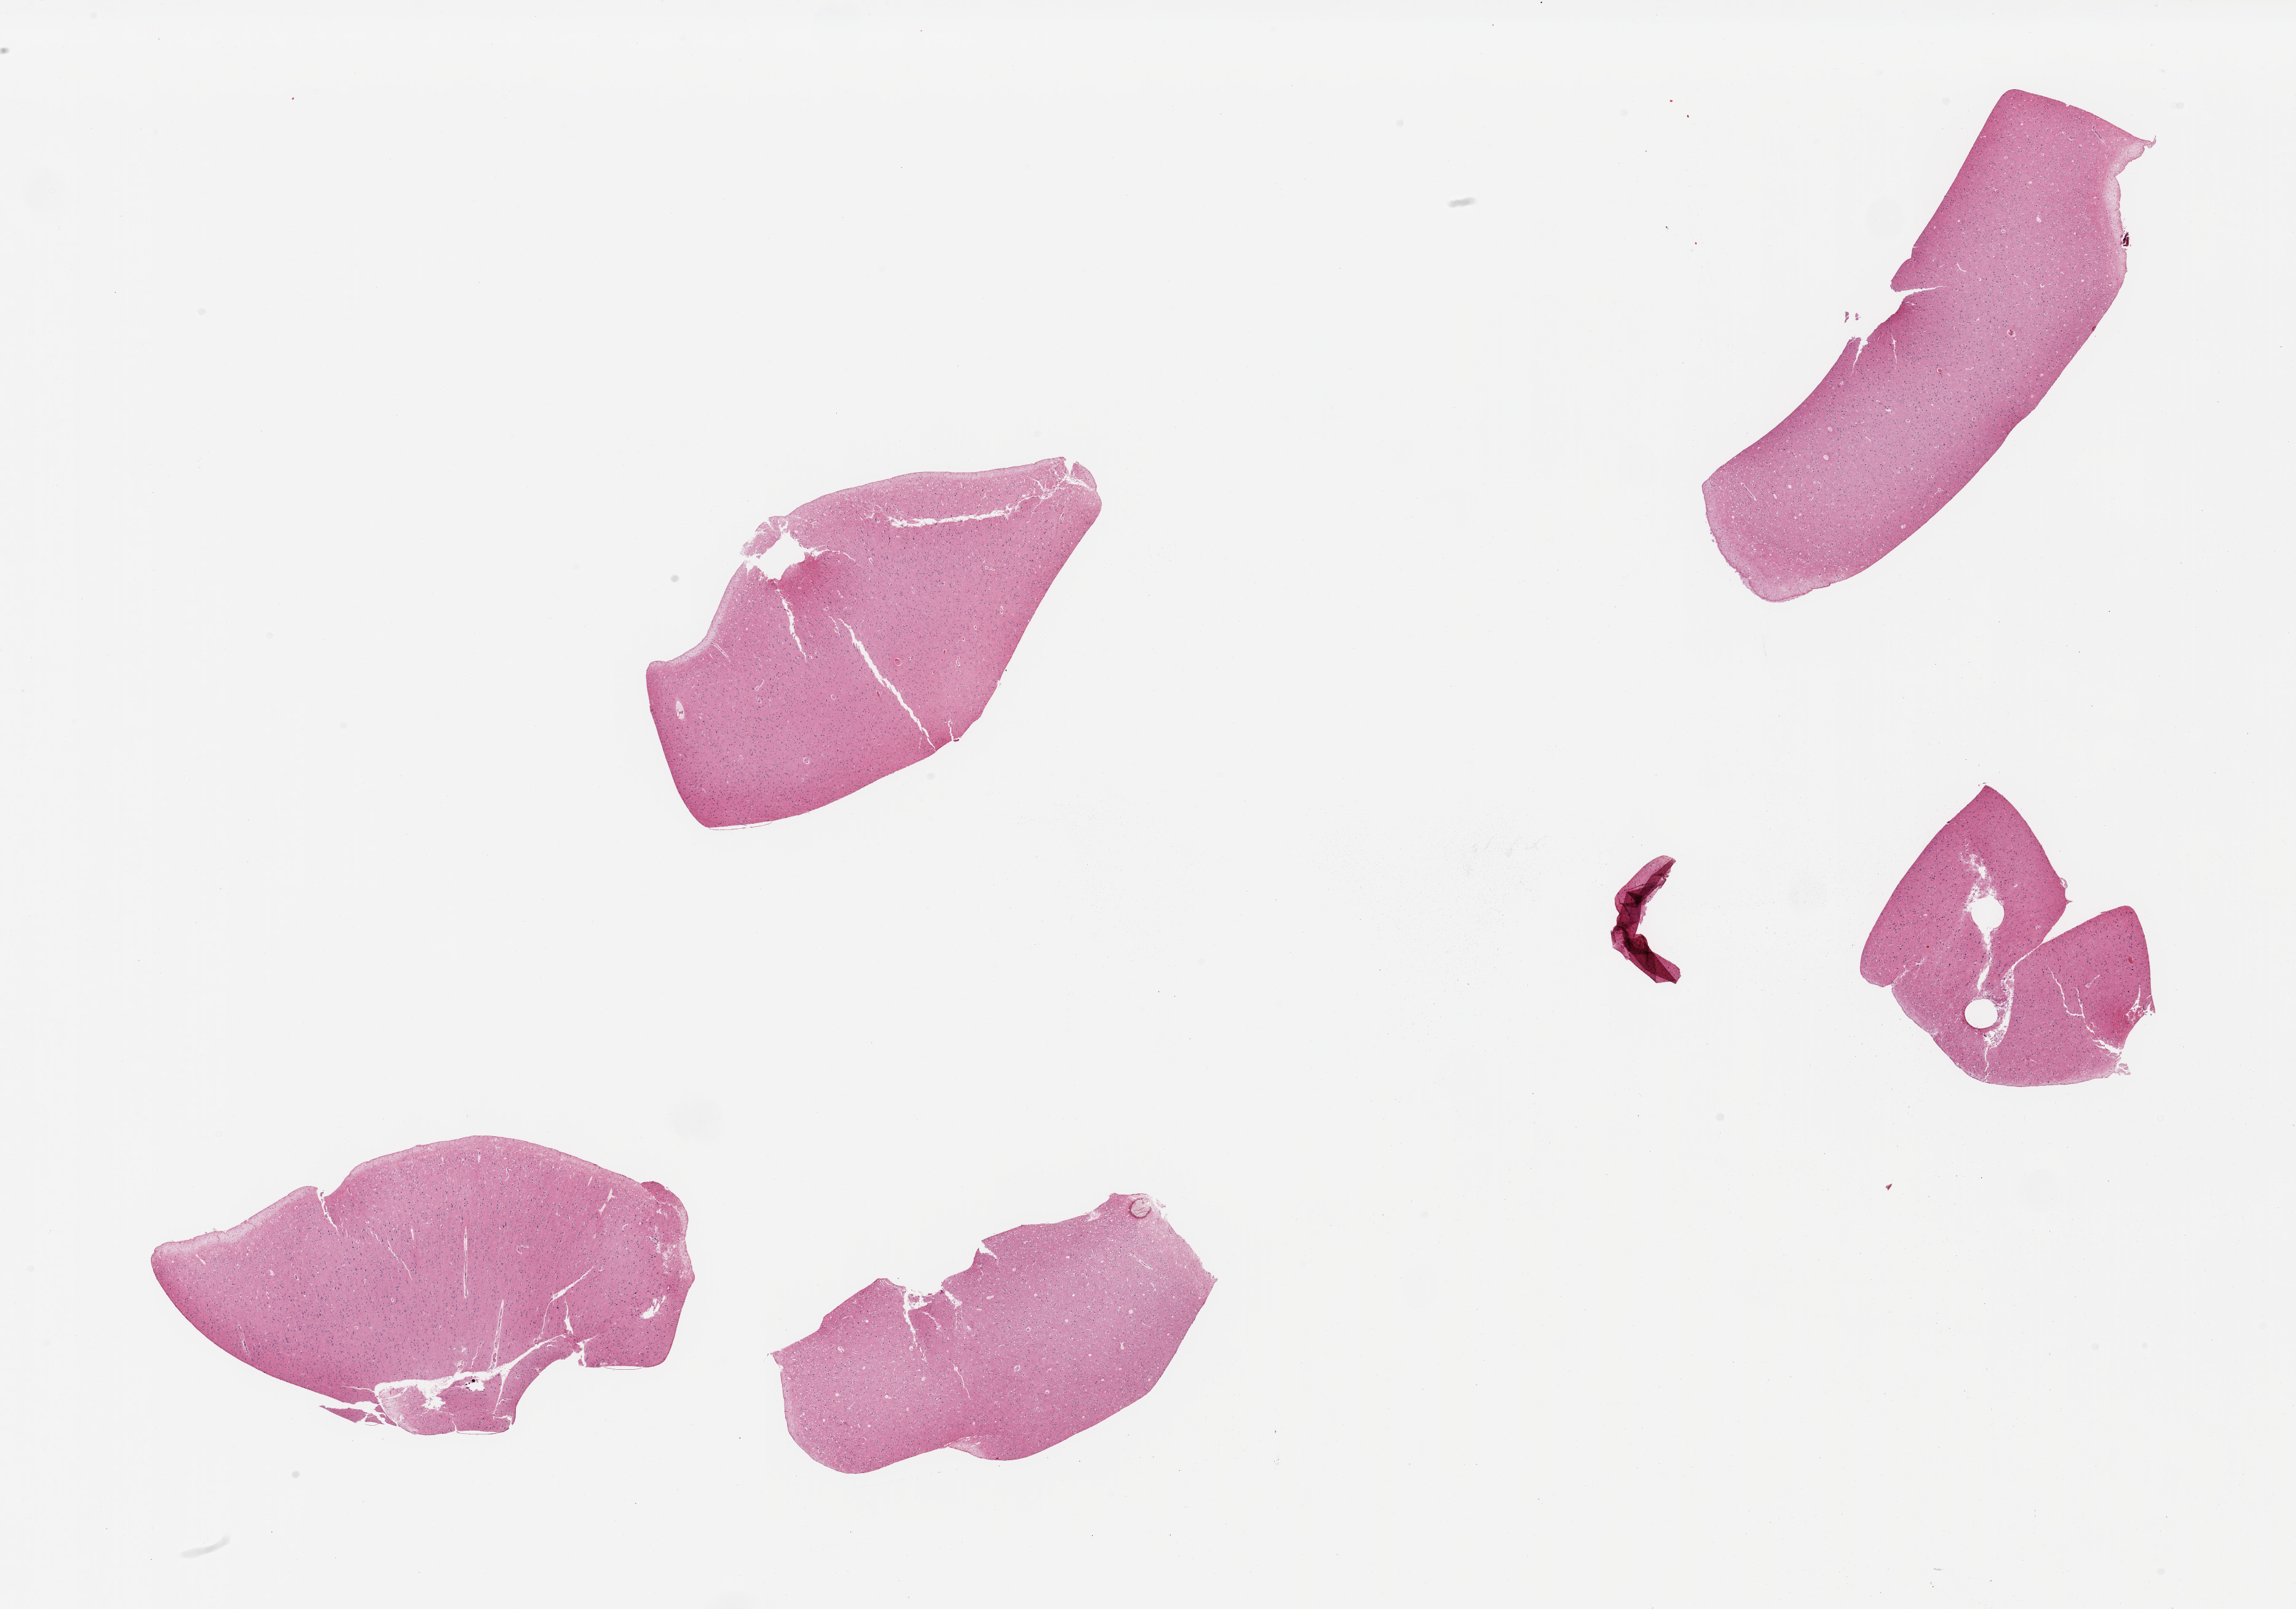
Whole-slide image, H&E stain — a low-resolution overview of the entire scanned area, about 29.5 x 20.7 mm, PAXgene-fixed paraffin-embedded (PFPE) section, sampled site (target tissue): cerebral cortex, tissue donor sample. Donor sex: male.
• reviewer comment on this tissue sample: 5 pieces, no abnormalities